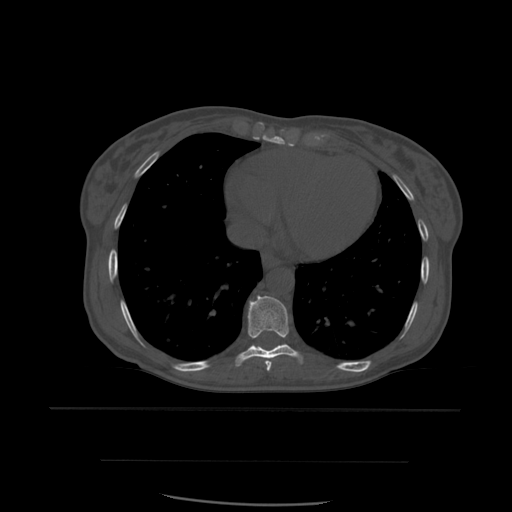
CT including the spine, one axial slice. Position 337 of 574 along the scan axis. Bone window (W 1800 / L 400 HU). 1.25 mm slice thickness. 512 × 512 image matrix, field of view 392 × 392 mm. Patient age 48 years. From the clinical record (not read from this slice): primary cancer: lung; vertebrae with lytic lesions (as recorded): T11.
Annotated regions visible in this slice (semi-automatic segmentation, software-assisted and operator-edited):
- T8 vertebra: bounding box [x1, y1, x2, y2] px = [265, 361, 272, 372]
- T9 vertebra: [235, 296, 304, 367]